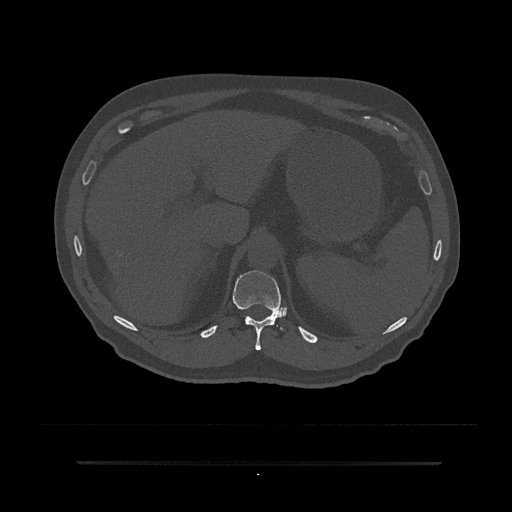
CT including the spine, one axial slice; slice 263 of 797 in the series (ordered by position); bone window (W 1800 / L 400 HU); 0.5 mm slice thickness; 512 × 512 image matrix, field of view 464 × 464 mm. Male patient, age 59 years. Case-level facts recorded for this patient, not image findings: primary cancer: bile ducts; vertebrae with lytic lesions (as recorded): T10.
Annotated regions visible in this slice (semi-automatic segmentation, software-assisted and operator-edited):
- T11 vertebra: box from (x=233, y=270) to (x=284, y=351) px